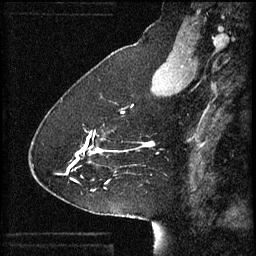
Breast MRI (dynamic contrast-enhanced), one sagittal slice. Position 20 of 60 along the scan axis. 3 images stored at this slice position (order not interpretable as contrast timing). 1.5 T. TE 4.2 ms, TR 8.2 ms. 2 mm slice thickness. 256 × 256 image matrix. Patient: female, 41 years.
Structures marked on this image (semi-automatically segmented with operator editing):
- analysis volume of interest (the breast-tissue region the enhancement analysis was run in; not a lesion): bounding box <68,132,120,181> (left, top, right, bottom; pixels)
- tumour enhancement mask (voxels above the 70 % enhancement threshold inside the analysis volume of interest): <68,132,117,181>